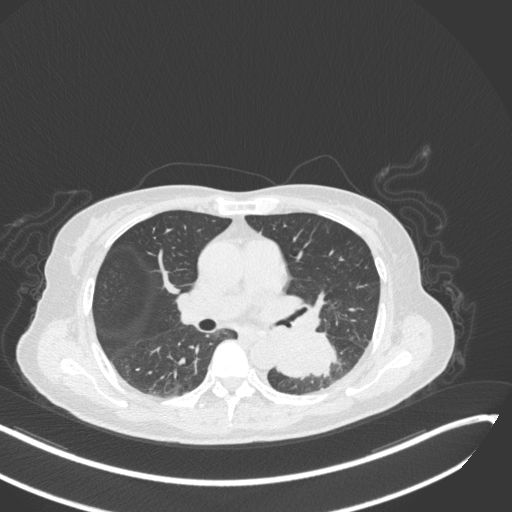
Chest CT, one axial slice. Position 155 of 342 along the scan axis. Reconstruction kernel B31f. 120 kVp. Lung window (W 1500 / L -600 HU). 512 × 512 image matrix. Female patient, age 64 years. From the clinical record (not read from this slice): clinical TNM (as recorded): T3 N1 M1; histopathological grade: G3.
Structures marked on this image (bounding box drawn by a radiologist):
- lung tumour (recorded histology: small cell carcinoma): bounding box <276,329,344,385> (left, top, right, bottom; pixels)